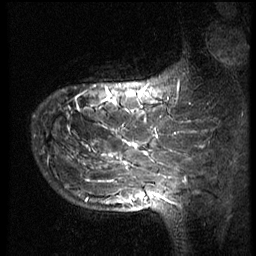
Breast MRI (dynamic contrast-enhanced), one sagittal slice. Position 17 of 66 along the scan axis. 3 images stored at this slice position (order not interpretable as contrast timing). 1.5 T. TE 4.2 ms, TR 8.9 ms. 2.5 mm slice thickness. 256 × 256 image matrix, field of view 200 × 200 mm. Female patient, age 39 years. From the clinical record (not read from this slice): setting: breast cancer imaged before/during neoadjuvant chemotherapy; receptor status: HER2-positive.
Outlined on this slice (semi-automatic segmentation, software-assisted and operator-edited):
- analysis volume of interest (the breast-tissue region the enhancement analysis was run in; not a lesion): box from (x=32, y=61) to (x=166, y=196) px
- tumour enhancement mask (voxels above the 140 % enhancement threshold inside the analysis volume of interest): (x=86, y=89)–(x=158, y=195)